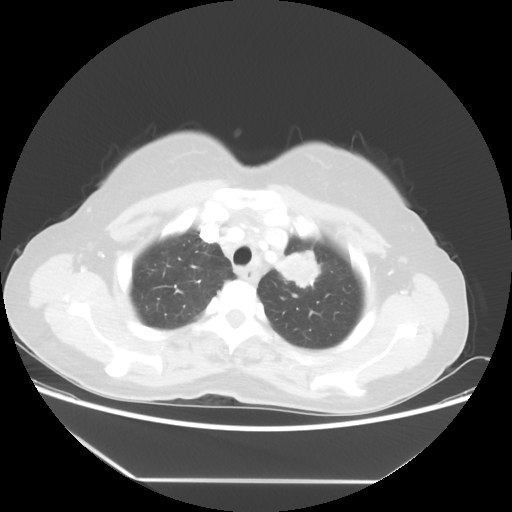
Chest CT, one axial slice; slice 44 of 52 in the series (ordered by position); 100 kVp; lung window (W 1500 / L -600 HU); 5 mm slice thickness; 512 × 512 image matrix, field of view 390 × 390 mm. Patient: female, 50 years. Case-level facts recorded for this patient, not image findings: clinical TNM (as recorded): T2 N3 M0.
Annotated regions visible in this slice (bounding box drawn by a radiologist):
- lung tumour (recorded histology: adenocarcinoma): bounding box (x1, y1, x2, y2) in pixels: (270, 239, 322, 296)